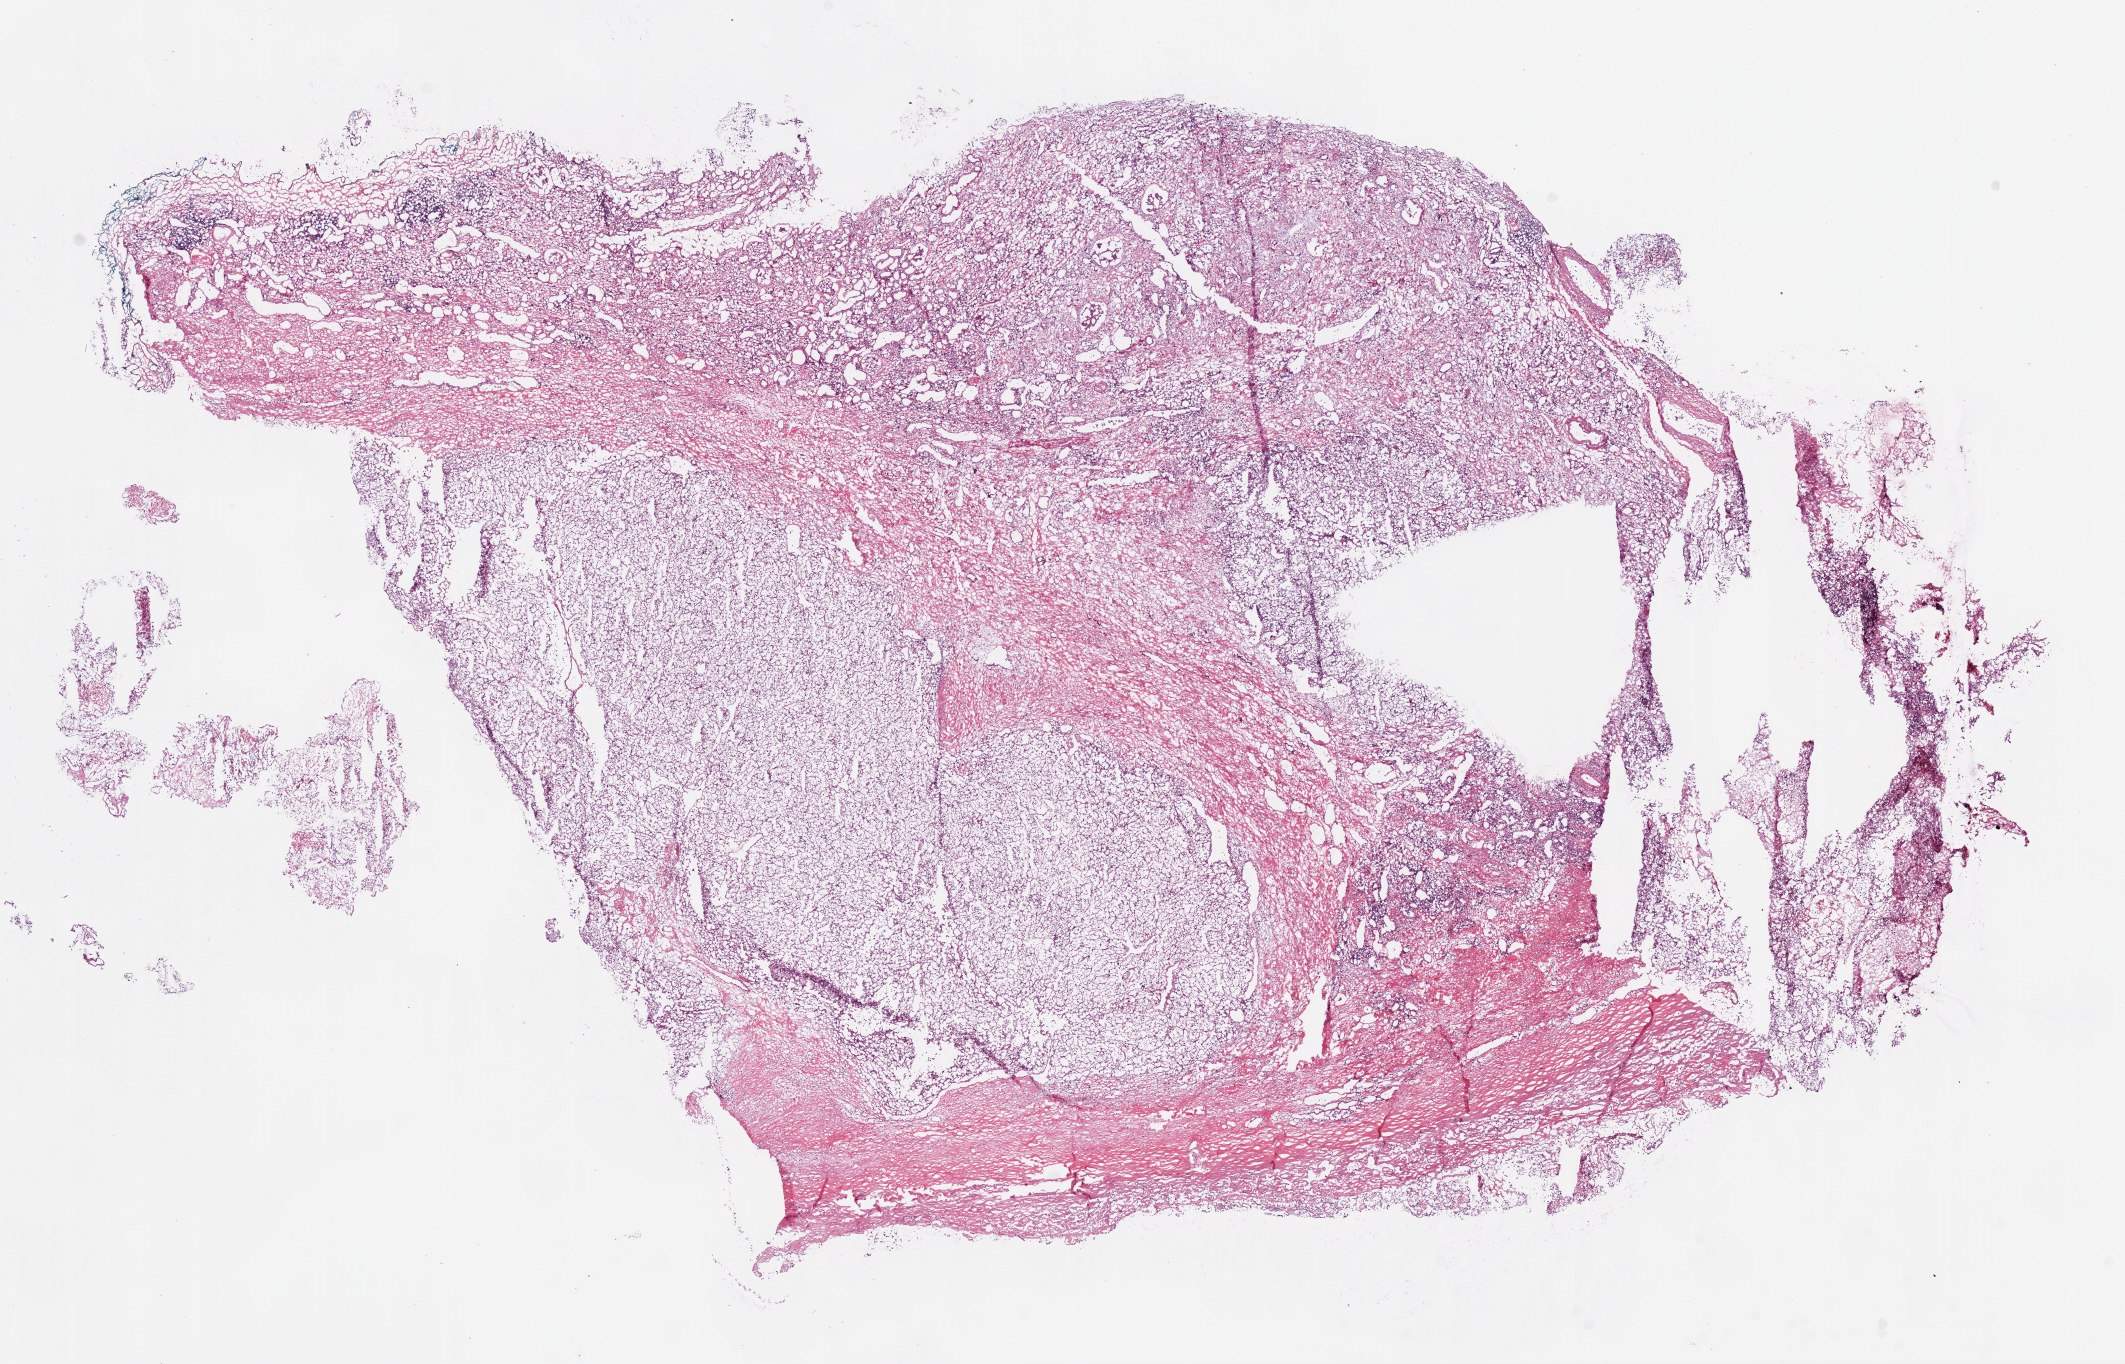
Digitized H&E tissue section (whole slide), low-resolution overview of the scanned area, about 17.1 x 10.9 mm (slide scanned at 20x), frozen section, sample: primary tumour, kidney. Patient: male, age at initial diagnosis 59 years. Histologic grade: G2 (moderately differentiated). Slide review estimates, as recorded: tumour cells 80%, tumour nuclei 90%, normal cells 0%, stromal cells 0%, necrosis 20%.
Diagnosis: Clear cell adenocarcinoma, NOS. AJCC pathologic stage: I (6th edition).